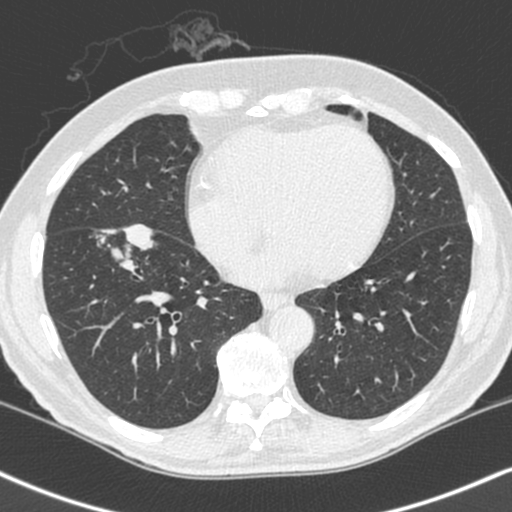
Chest CT (low-dose screening protocol), one axial image, baseline annual screen, lung window (W 1500 / L -600 HU), 1.3 mm slice thickness, slice 146 of 248 in the series. Male participant, aged 68 years at enrolment.
Expert reader's lesion annotation, bounding box (x1, y1, x2, y2) in pixels: (86, 221, 161, 292). Screening reader's record for this exam (one nodule recorded; not confirmed to be the boxed lesion): non-calcified nodule or mass ≥4 mm, right lower lobe, 34 × 17 mm, smooth margins, soft tissue attenuation. Later outcome: lung cancer diagnosed 24 days after this screen — combined small cell carcinoma, right lower lobe, stage IIIA (AJCC 6th edition), 41 mm at pathology.